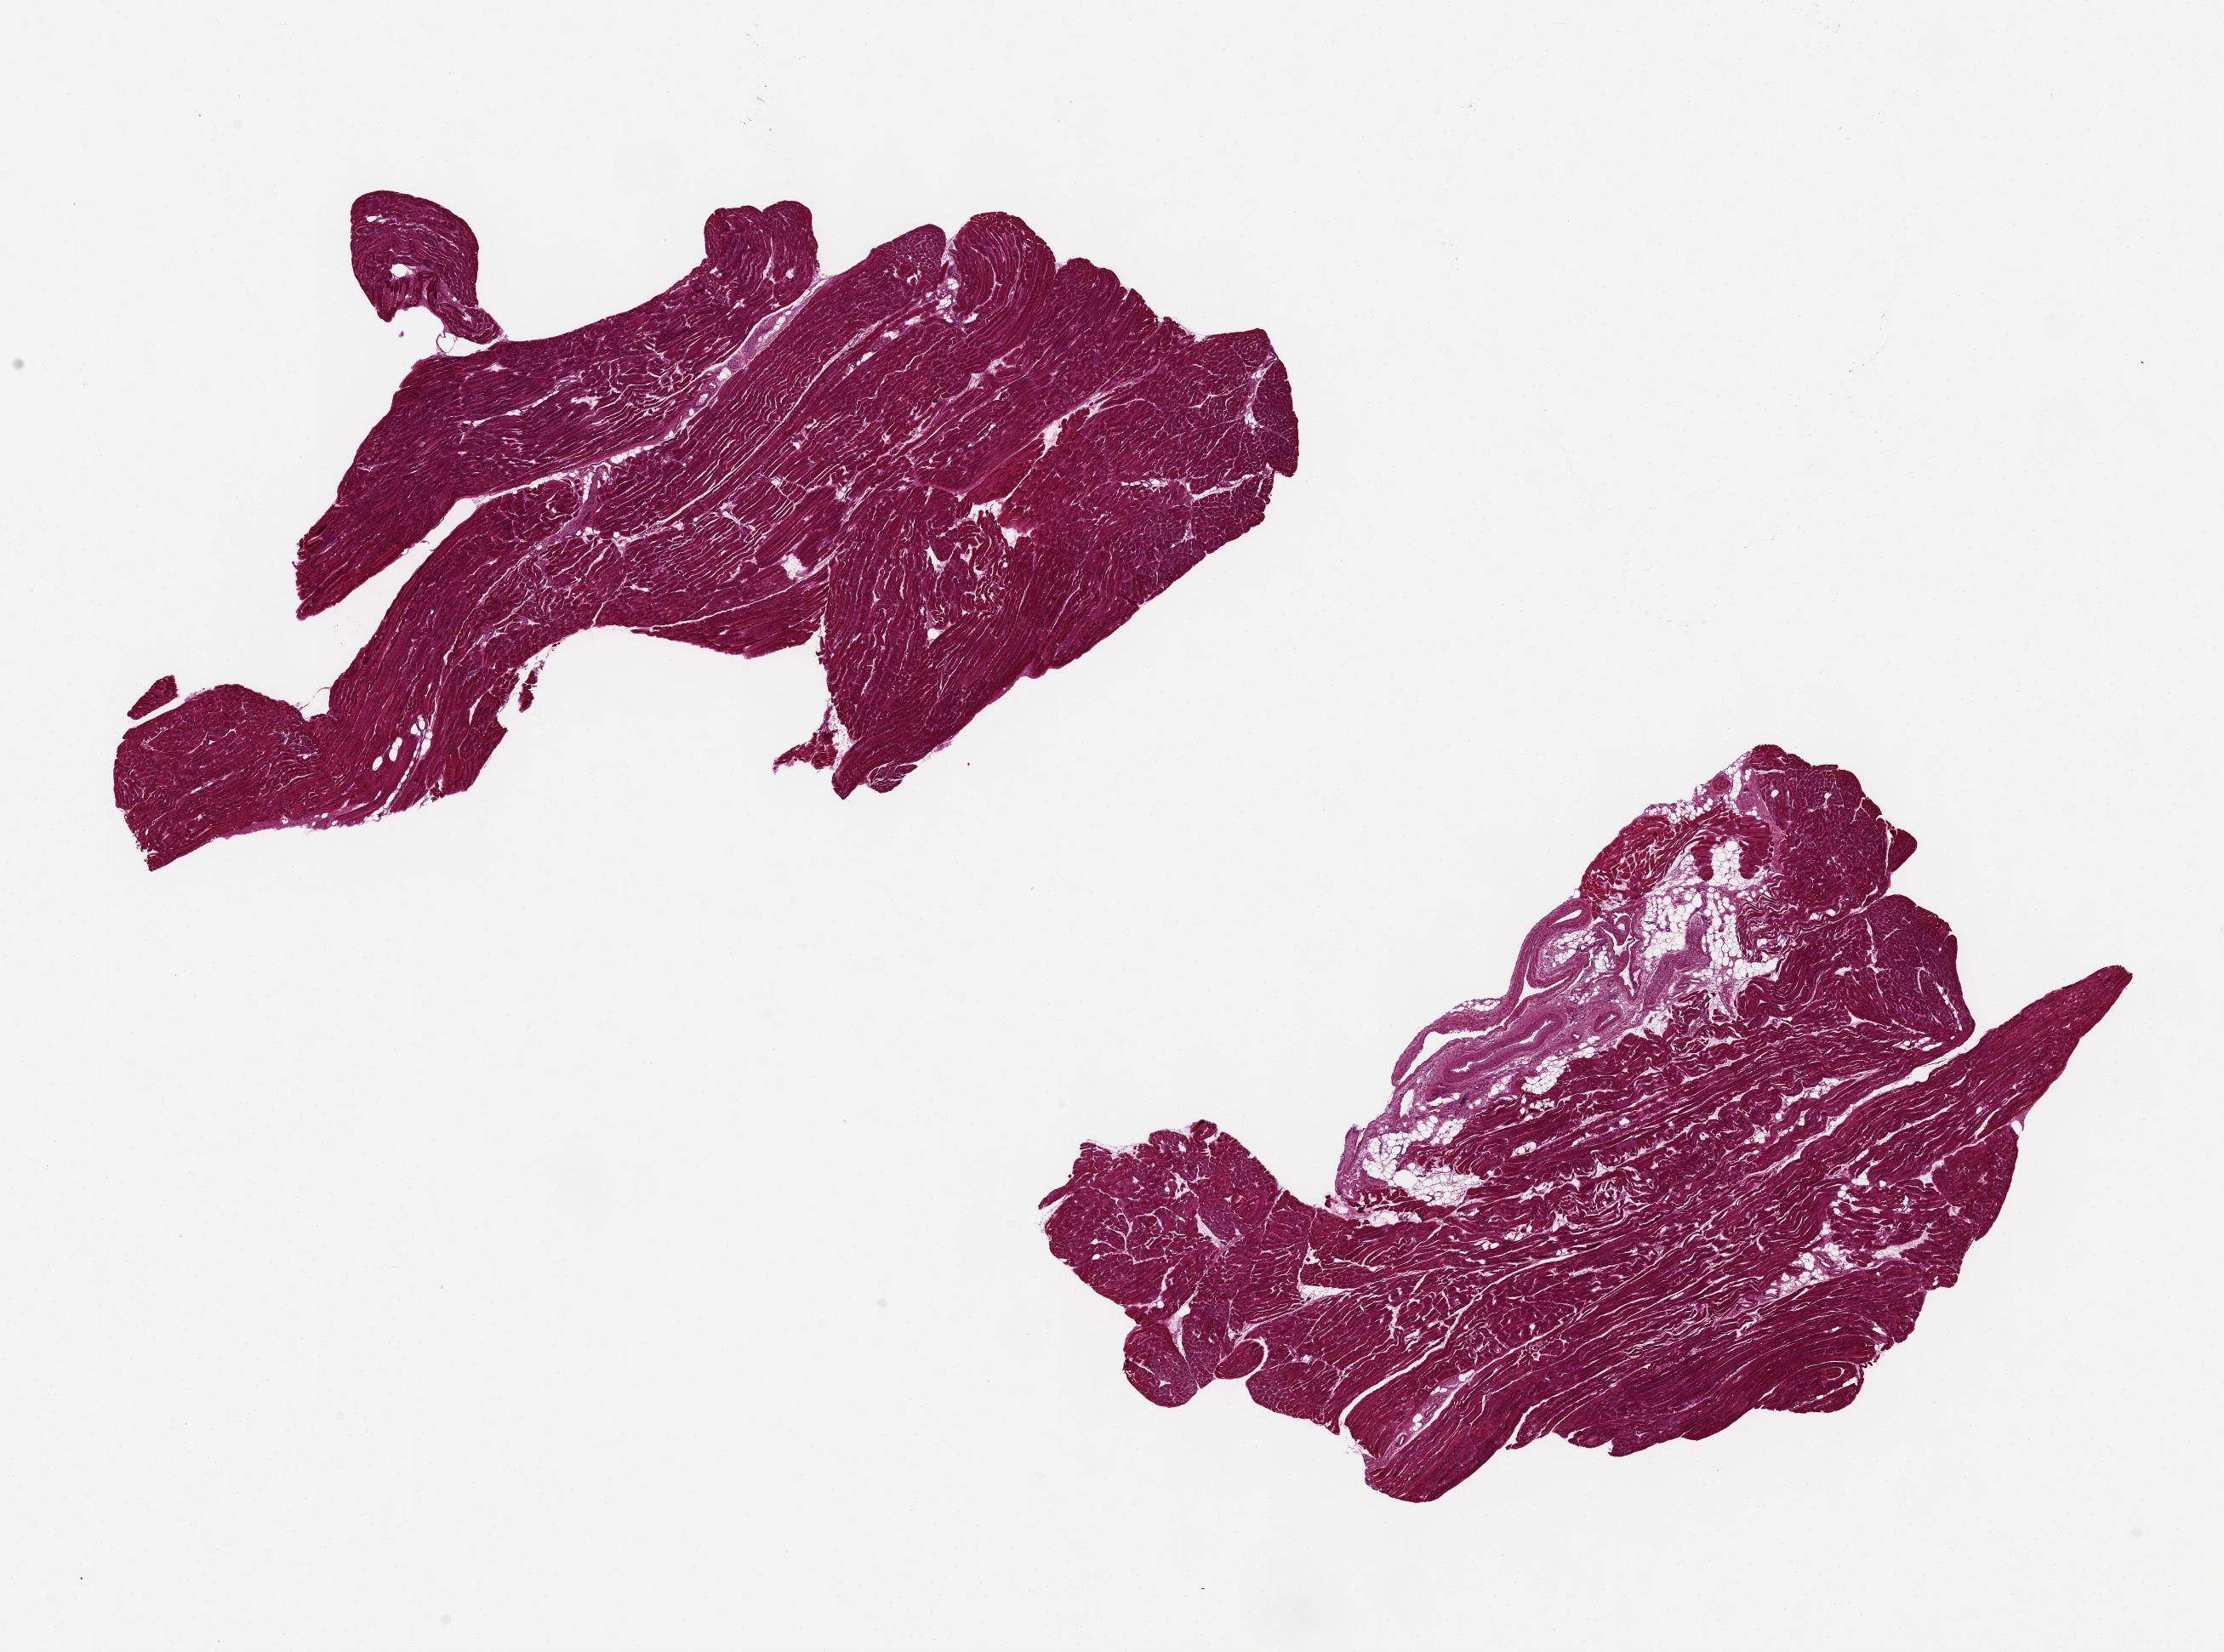
Whole-slide image, hematoxylin and eosin (H&E) stain, brightfield, low-resolution overview of the scanned area, about 20.7 x 15.4 mm (slide scanned at 20x). PAXgene-fixed paraffin-embedded (PFPE) section. Target tissue: skeletal muscle. Tissue donor sample. Female donor.
* reviewer comment on this tissue sample: 2 pieces 11x5 & 8.6x5 mm; 1 with ~10% adipose and adjacent blood vessels and nerve